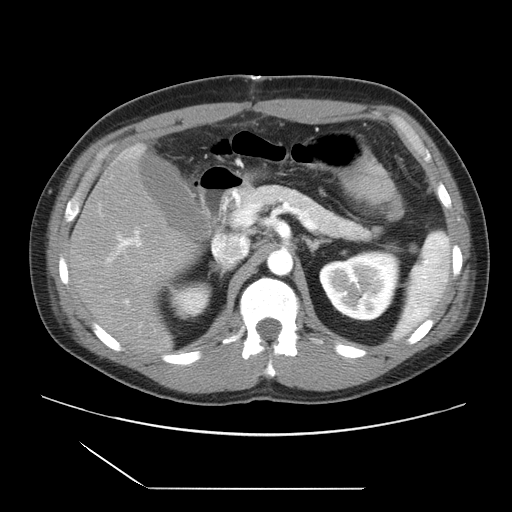
Contrast-enhanced abdominal CT, one axial slice. Position 13 of 39 along the scan axis. Intravenous contrast given. Soft-tissue window (W 400 / L 40 HU). 5 mm slice thickness. 512 × 512 image matrix, field of view 395 × 395 mm. Male patient, age 39 years. From the clinical record (not read from this slice): diagnosis: colorectal cancer liver metastases, imaged before liver resection; multiple liver metastases: yes.
Structures marked on this image (expert manual segmentation):
- hepatic veins: bounding box <216,235,243,263> (left, top, right, bottom; pixels)
- liver: <68,148,197,356>
- portal vein (with intrahepatic branches): <105,203,240,305>